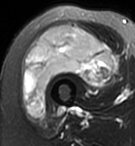
MRI of an extremity soft-tissue mass, one axial slice. Slice 37 of 95 in the series (ordered by position). T2-weighted fat-saturated. MR volume resampled by the dataset authors to the PET/CT grid (not the native acquisition matrix). 3.27 mm slice thickness. 135 × 146 image matrix. Female patient. Case-level facts recorded for this patient, not image findings: histological type: pleiomorphic undifferentiated sarcoma; grade: high; site of the primary tumour: right quadricep.
Outlined on this slice (expert contour drawn on MRI and transferred to this co-registered scan by the dataset authors):
- gross tumour volume including surrounding oedema: box from (x=23, y=27) to (x=113, y=117) px
- gross tumour volume (mass): (x=23, y=27)–(x=113, y=117)